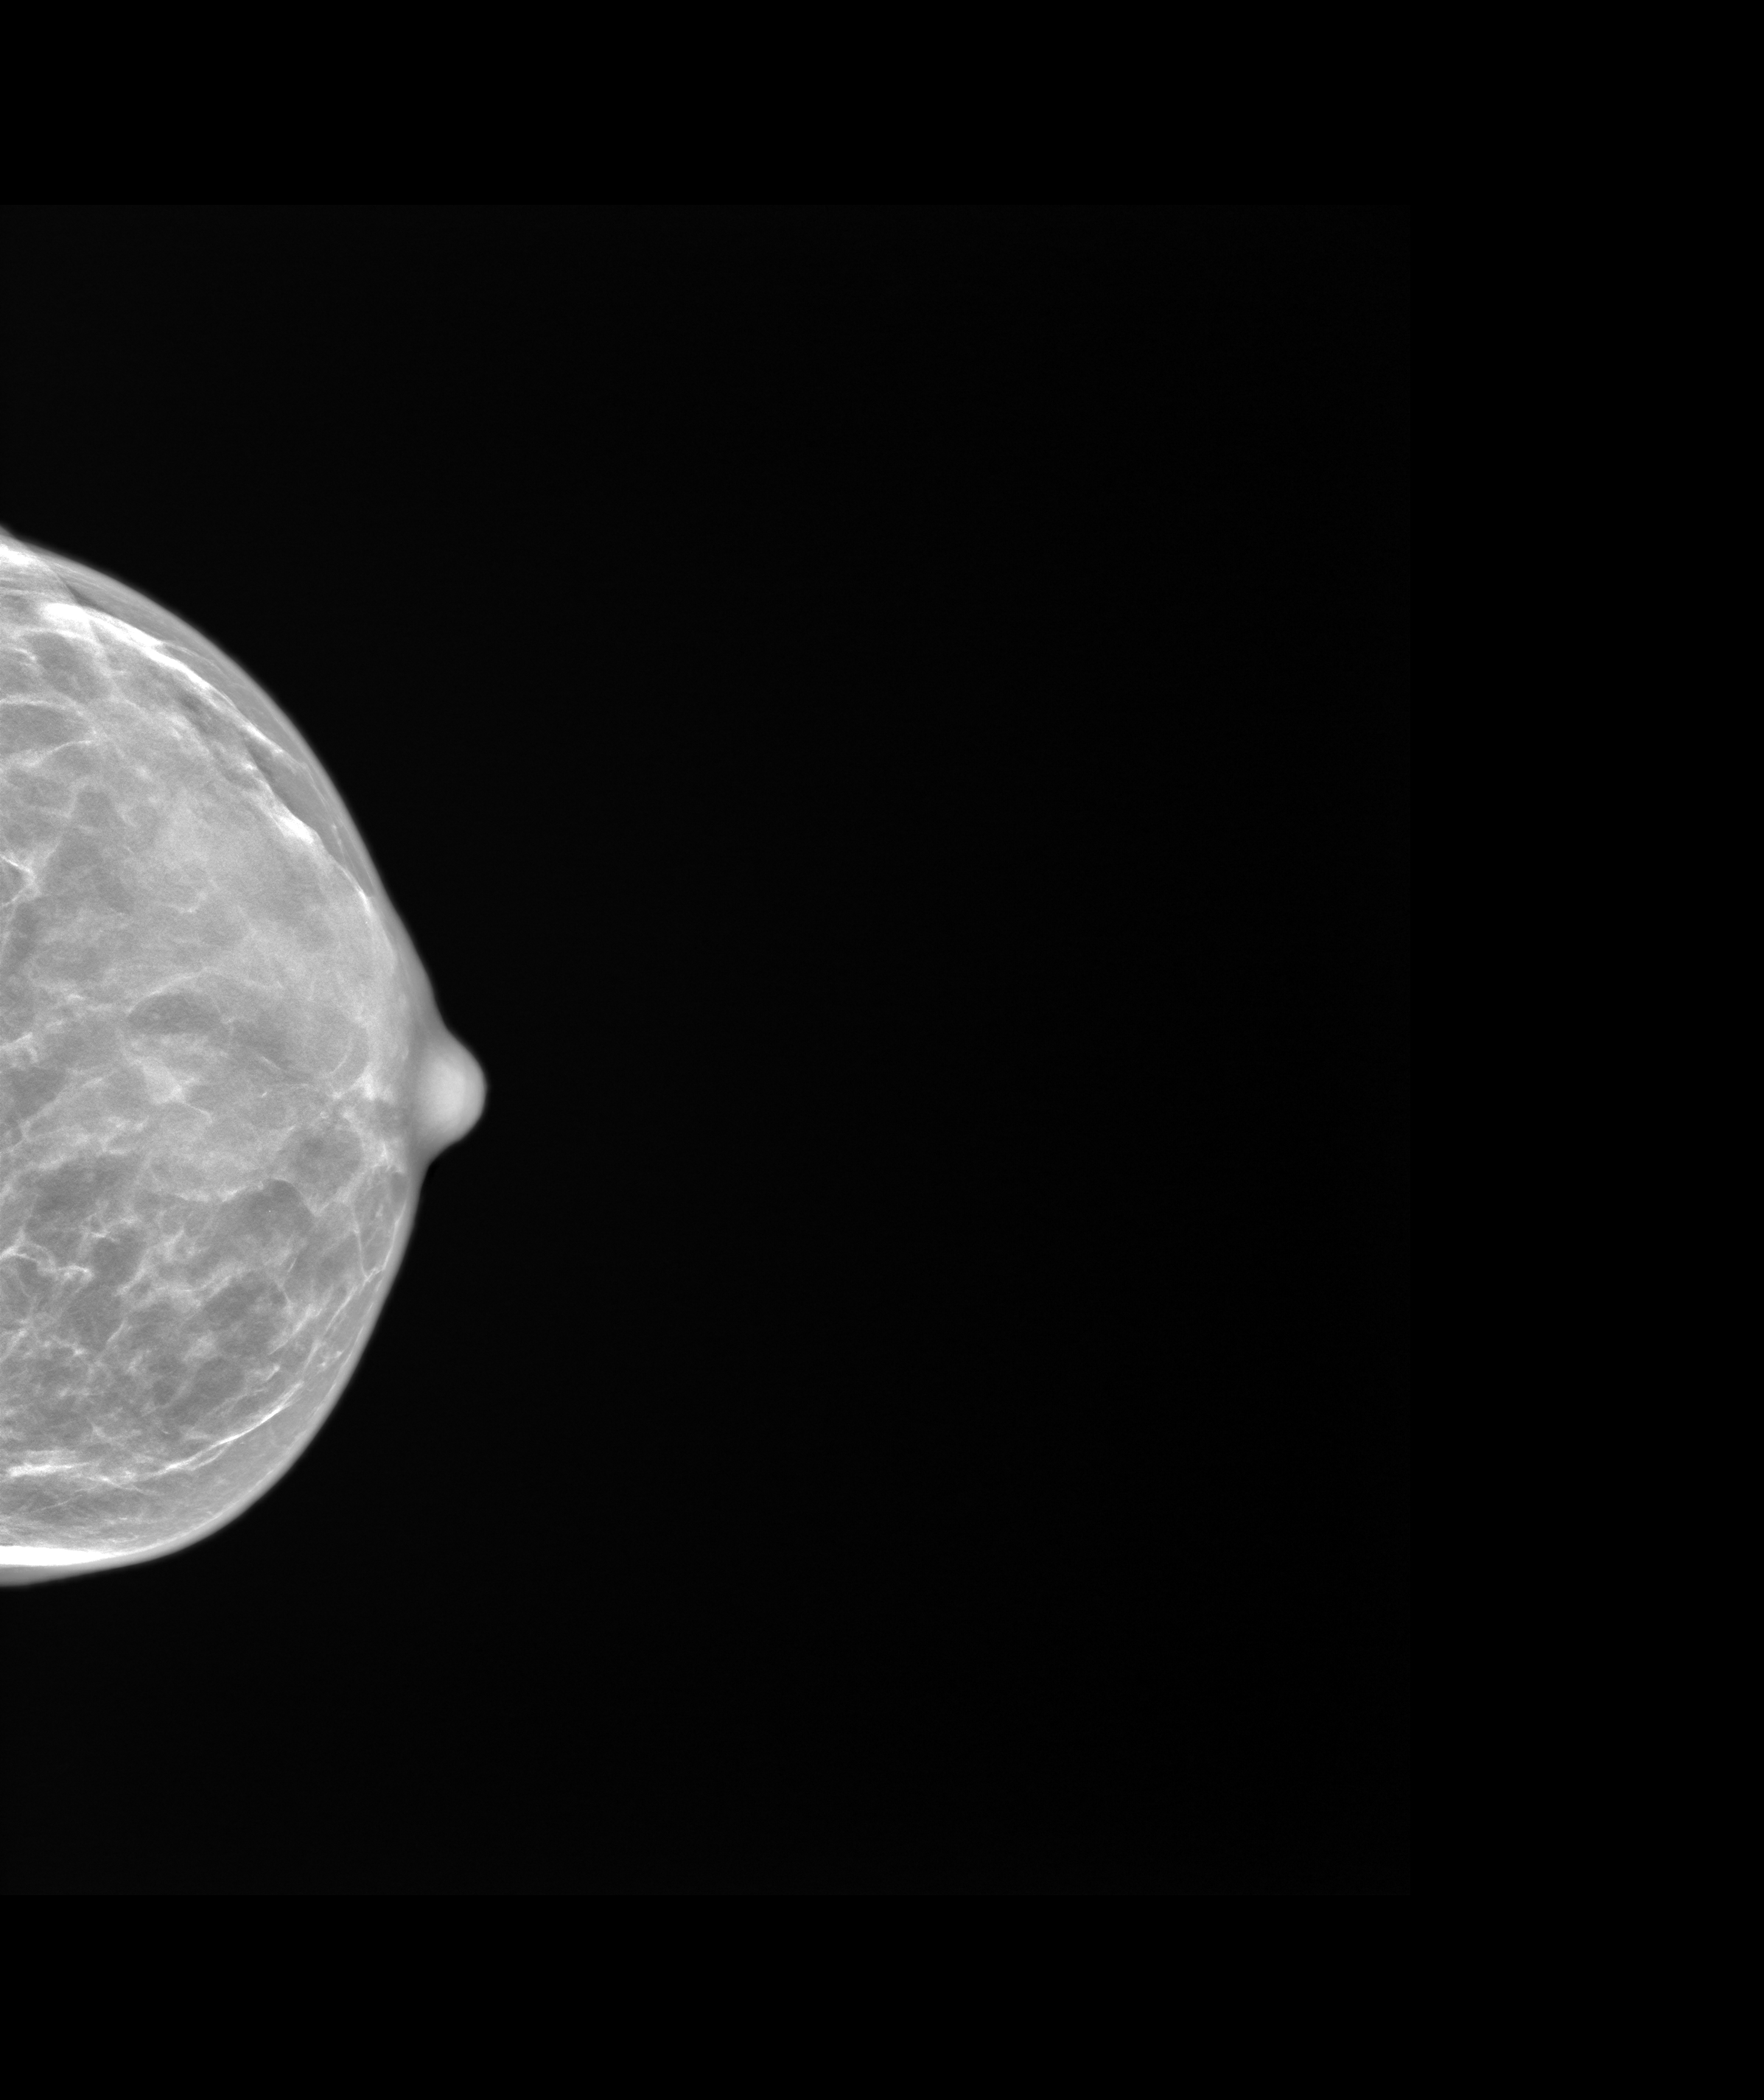
Annual screening mammography examination. Patient aged 55 years (female).
Image type: synthesized 2-D view from tomosynthesis. Breast: left. Projection: craniocaudal (CC) view.